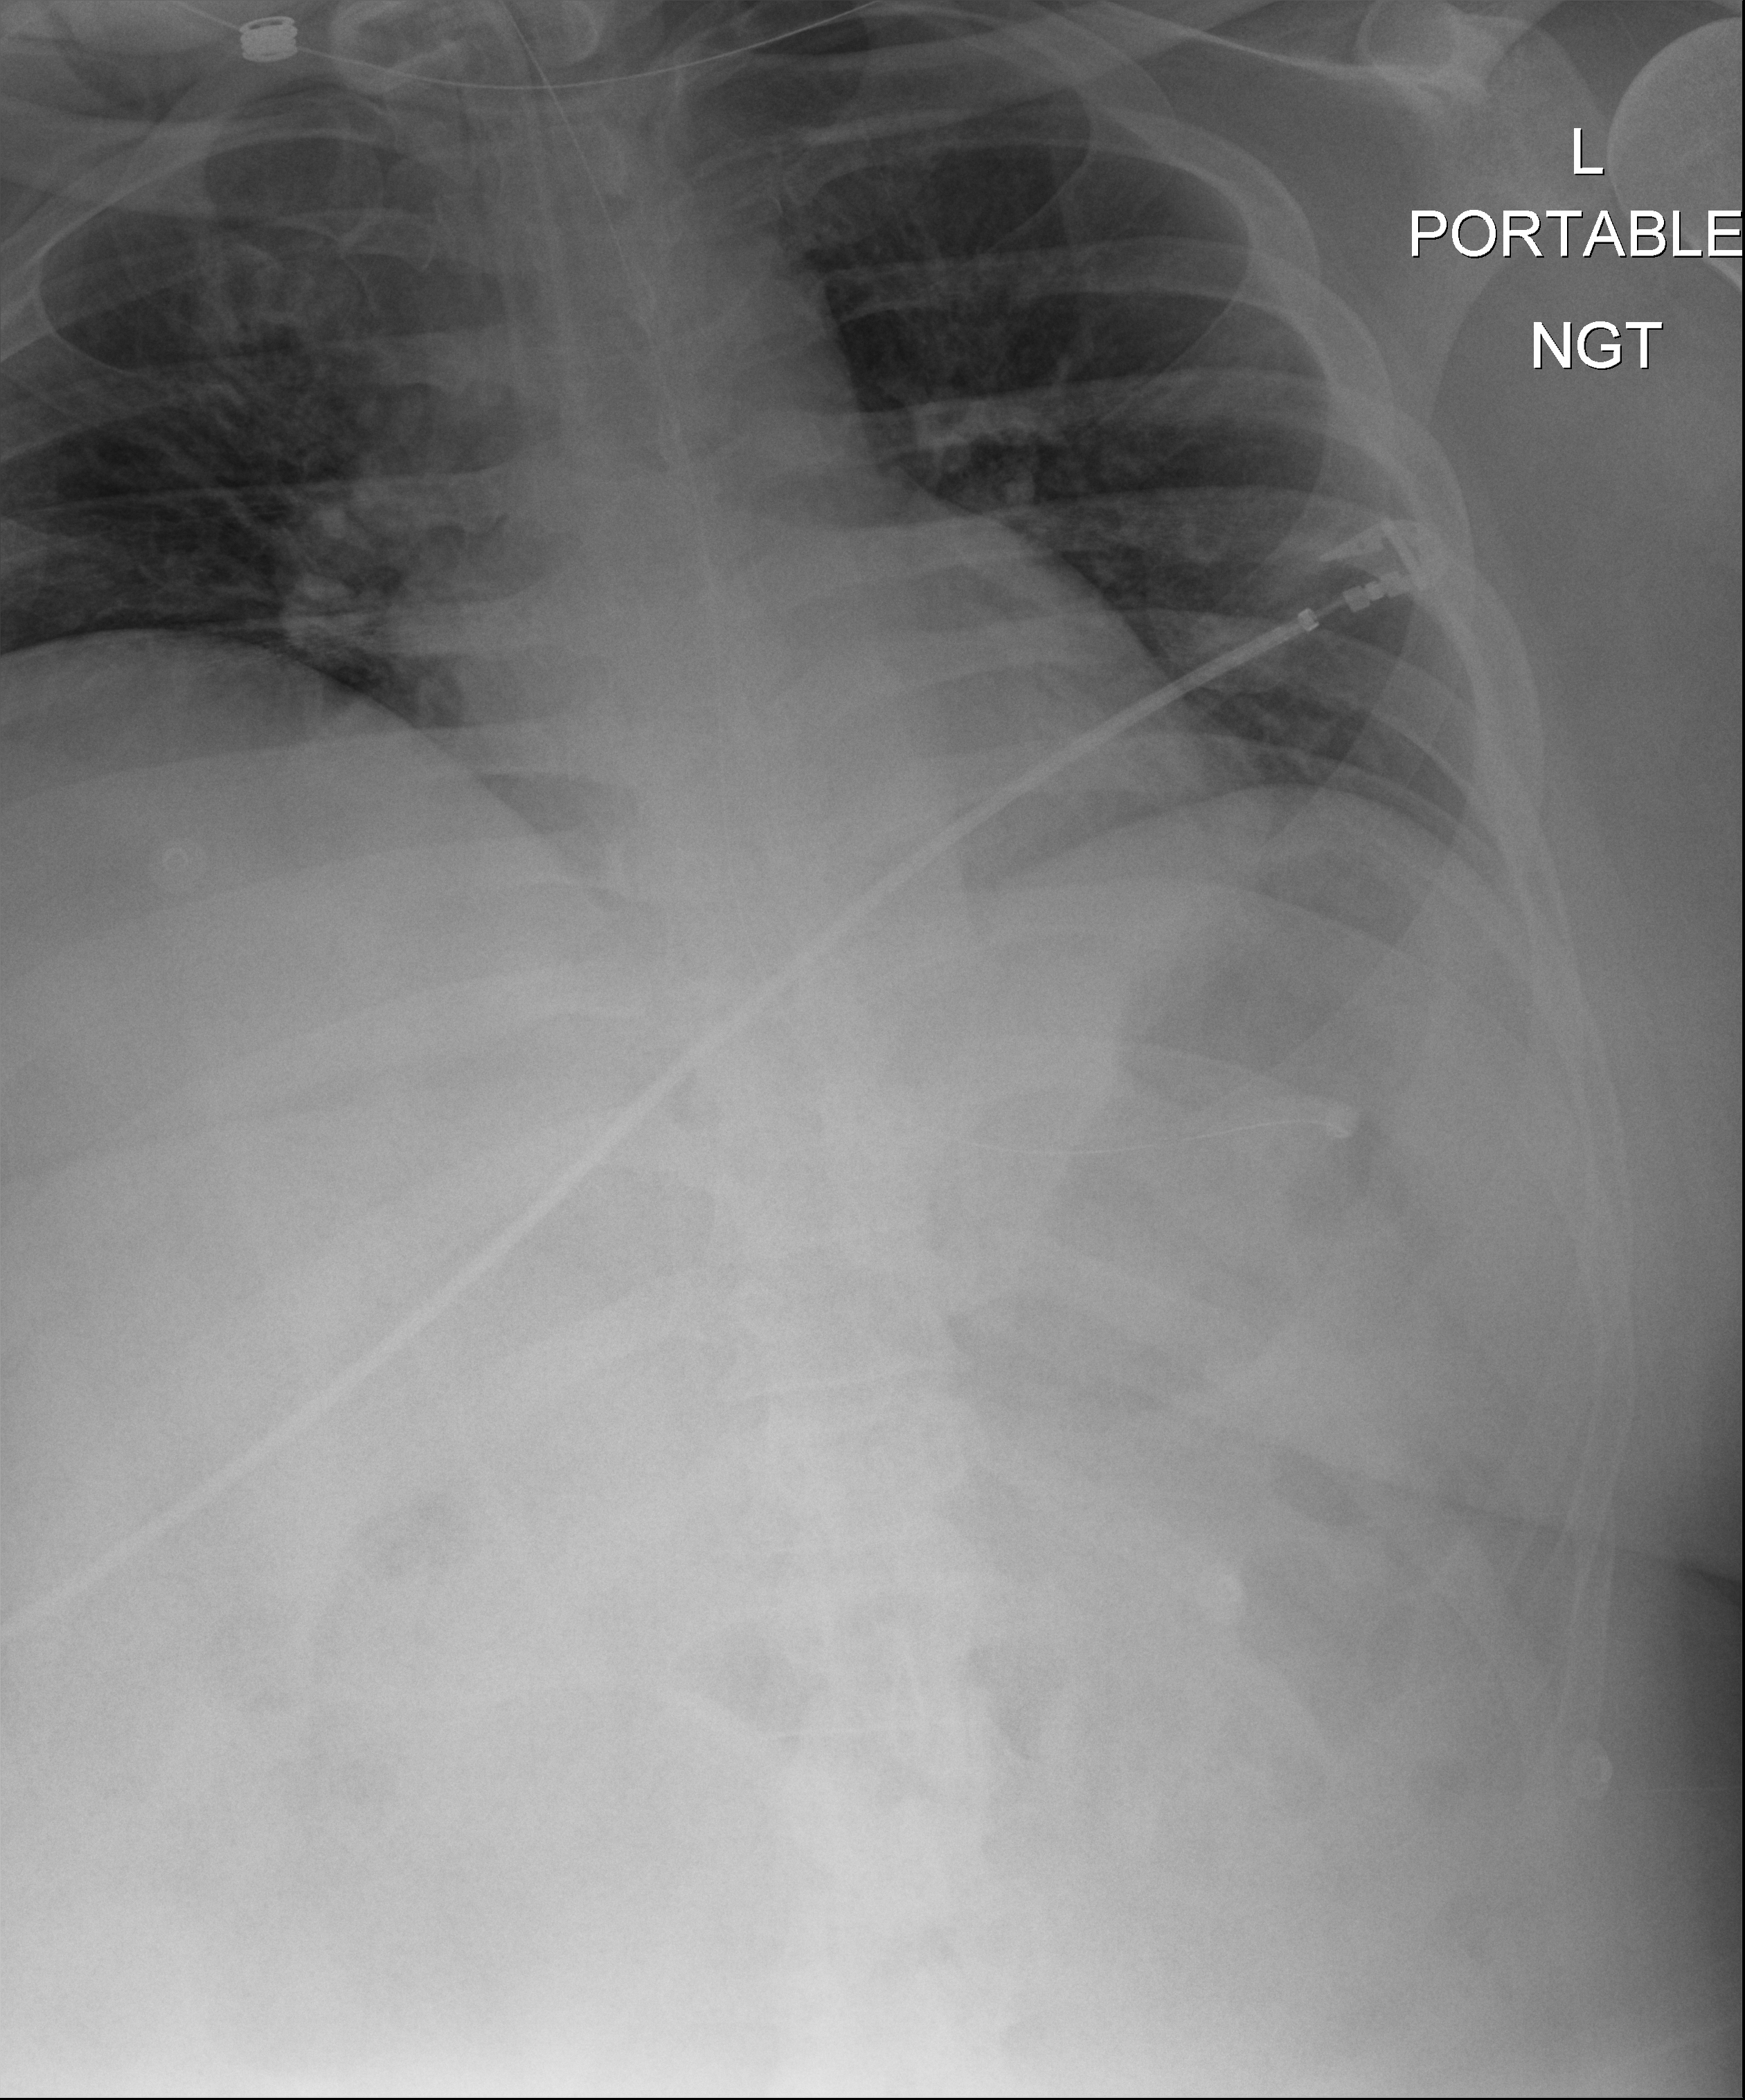
Chest X-ray (portable), anteroposterior (AP) projection. Male patient hospitalised with COVID-19, age 18–59 years.
From the hospital-stay record, not from the radiograph (when in the stay this image was taken is not recorded):
- mechanically ventilated during this hospital stay: yes